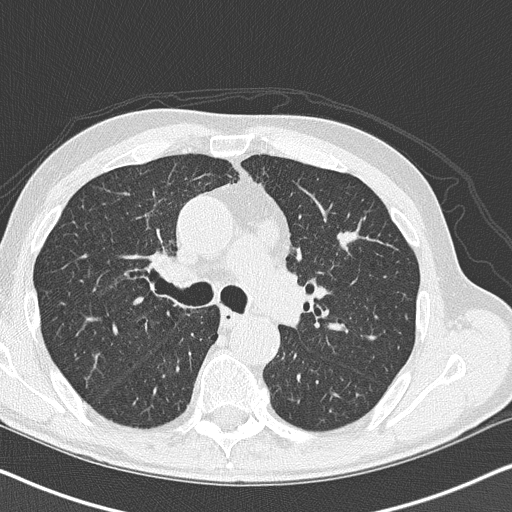
Low-dose screening chest CT, one axial slice; position 102 of 158 along the scan axis; reconstruction kernel B50f; 120 kVp; lung window (W 1500 / L -600 HU); 2 mm slice thickness; 512 × 512 image matrix.
Outlined on this slice (manually delineated by an expert):
- lesion 1 (tumor, upper lobe of left lung): bounding box [x1, y1, x2, y2] px = [338, 231, 358, 248]